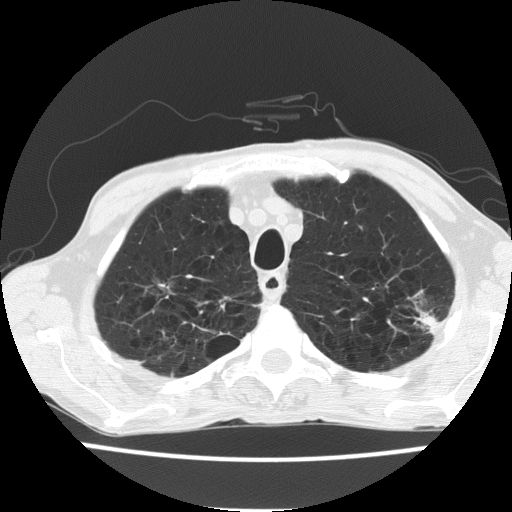
Chest CT (low-dose screening protocol), one axial image, baseline annual screen, lung window (W 1500 / L -600 HU), slice 33 of 187 in the series. Male participant, aged 60 years at enrolment.
Lesion marked by an expert reader, box from (x=396, y=289) to (x=456, y=348) px. Screening reader's record for this exam: no non-calcified nodule ≥4 mm recorded. Lung cancer was diagnosed 490 days after this screen (after the second annual screen): bronchiolo-alveolar carcinoma, mucinous, left upper lobe, stage IV (AJCC 6th edition).